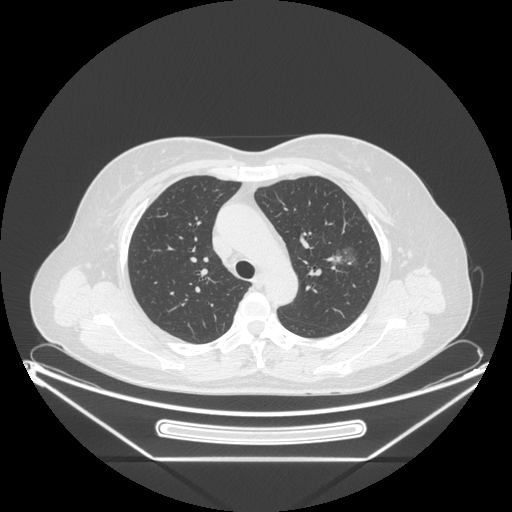
Chest CT, one axial slice. Reconstruction kernel STANDARD. 120 kVp. Lung window (W 1500 / L -600 HU). 1.25 mm slice thickness. 512 × 512 image matrix, field of view 447 × 447 mm. Female patient, age 54 years. From the clinical record (not read from this slice): clinical TNM (as recorded): T1c N0 M0; histopathological grade: G1.
Outlined on this slice (rectangle marked by the reading radiologist):
- lung tumour (recorded histology: adenocarcinoma): bounding box (x1, y1, x2, y2) in pixels: (325, 239, 374, 280)